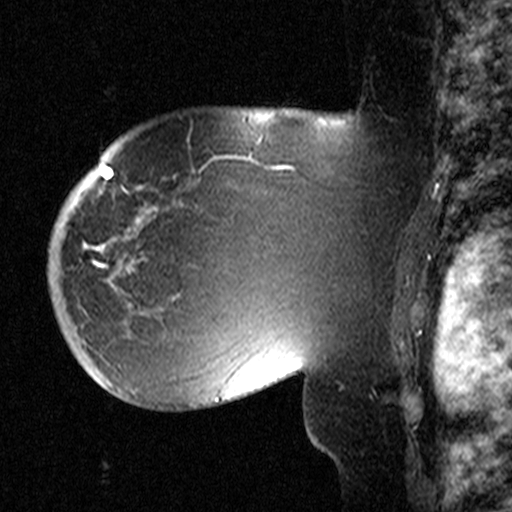
Breast MRI (dynamic contrast-enhanced), one sagittal slice; position 32 of 44 along the scan axis; dynamic contrast-enhanced study with each time point stored as its own series, time point 2 of 3 at this slice position (early post-contrast, ordered by acquisition time); 1.5 T; TE 4.5 ms, TR 11 ms; 512 × 512 image matrix, field of view 200 × 200 mm. Patient: female, 53 years. From the clinical record (not read from this slice): setting: breast cancer imaged before/during neoadjuvant chemotherapy; receptor status: HR-positive, HER2-negative.
Outlined on this slice (semi-automatically segmented with operator editing):
- analysis volume of interest (the breast-tissue region the enhancement analysis was run in; not a lesion): bounding box [x1, y1, x2, y2] px = [58, 154, 311, 367]
- tumour enhancement mask (voxels above the 90 % enhancement threshold inside the analysis volume of interest): [91, 228, 128, 267]